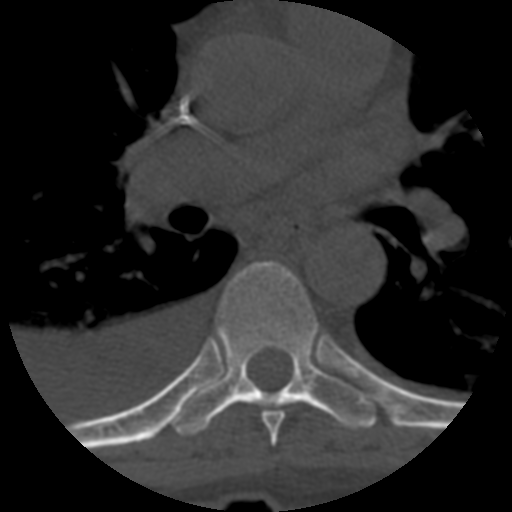
CT including the spine, one axial slice; reconstruction kernel STANDARD; 120 kVp; one of 3 acquisitions stored at this slice position; bone window (W 1800 / L 400 HU); 1.25 mm slice thickness; 512 × 512 image matrix. Patient age 55 years. From the clinical record (not read from this slice): primary cancer: colon.
Structures marked on this image (semi-automatically segmented with operator editing):
- T6 vertebra: bounding box (x1, y1, x2, y2) in pixels: (261, 408, 285, 446)
- T7 vertebra: (171, 261, 377, 437)